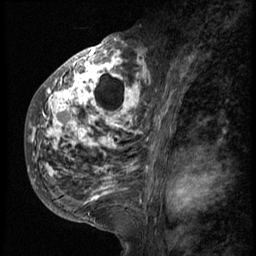
Breast MRI (dynamic contrast-enhanced), one sagittal slice; position 31 of 58 along the scan axis; 3 images stored at this slice position (order not interpretable as contrast timing); 1.5 T; TE 4.2 ms, TR 9 ms; 2.5 mm slice thickness; 256 × 256 image matrix, field of view 180 × 180 mm. Patient: female, 50 years. From the clinical record (not read from this slice): setting: breast cancer imaged before/during neoadjuvant chemotherapy; receptor status: triple-negative.
Structures marked on this image (semi-automatic segmentation, software-assisted and operator-edited):
- analysis volume of interest (the breast-tissue region the enhancement analysis was run in; not a lesion): box from (x=26, y=48) to (x=148, y=214) px
- tumour enhancement mask (voxels above the 140 % enhancement threshold inside the analysis volume of interest): (x=31, y=48)–(x=148, y=201)